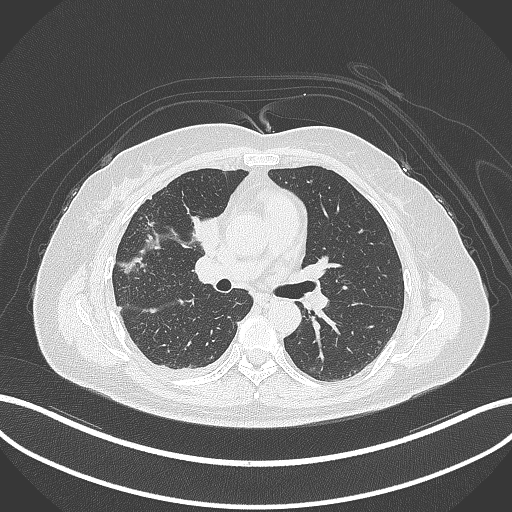
Chest CT, one axial slice. Position 155 of 305 along the scan axis. Reconstruction kernel B70f. 120 kVp. Lung window (W 1500 / L -600 HU). 1 mm slice thickness. 512 × 512 image matrix, field of view 400 × 400 mm. Female patient, age 52 years. From the clinical record (not read from this slice): clinical TNM (as recorded): T3 N1 M1.
Outlined on this slice (rectangle marked by the reading radiologist):
- lung tumour (recorded histology: adenocarcinoma): box from (x=183, y=210) to (x=220, y=258) px